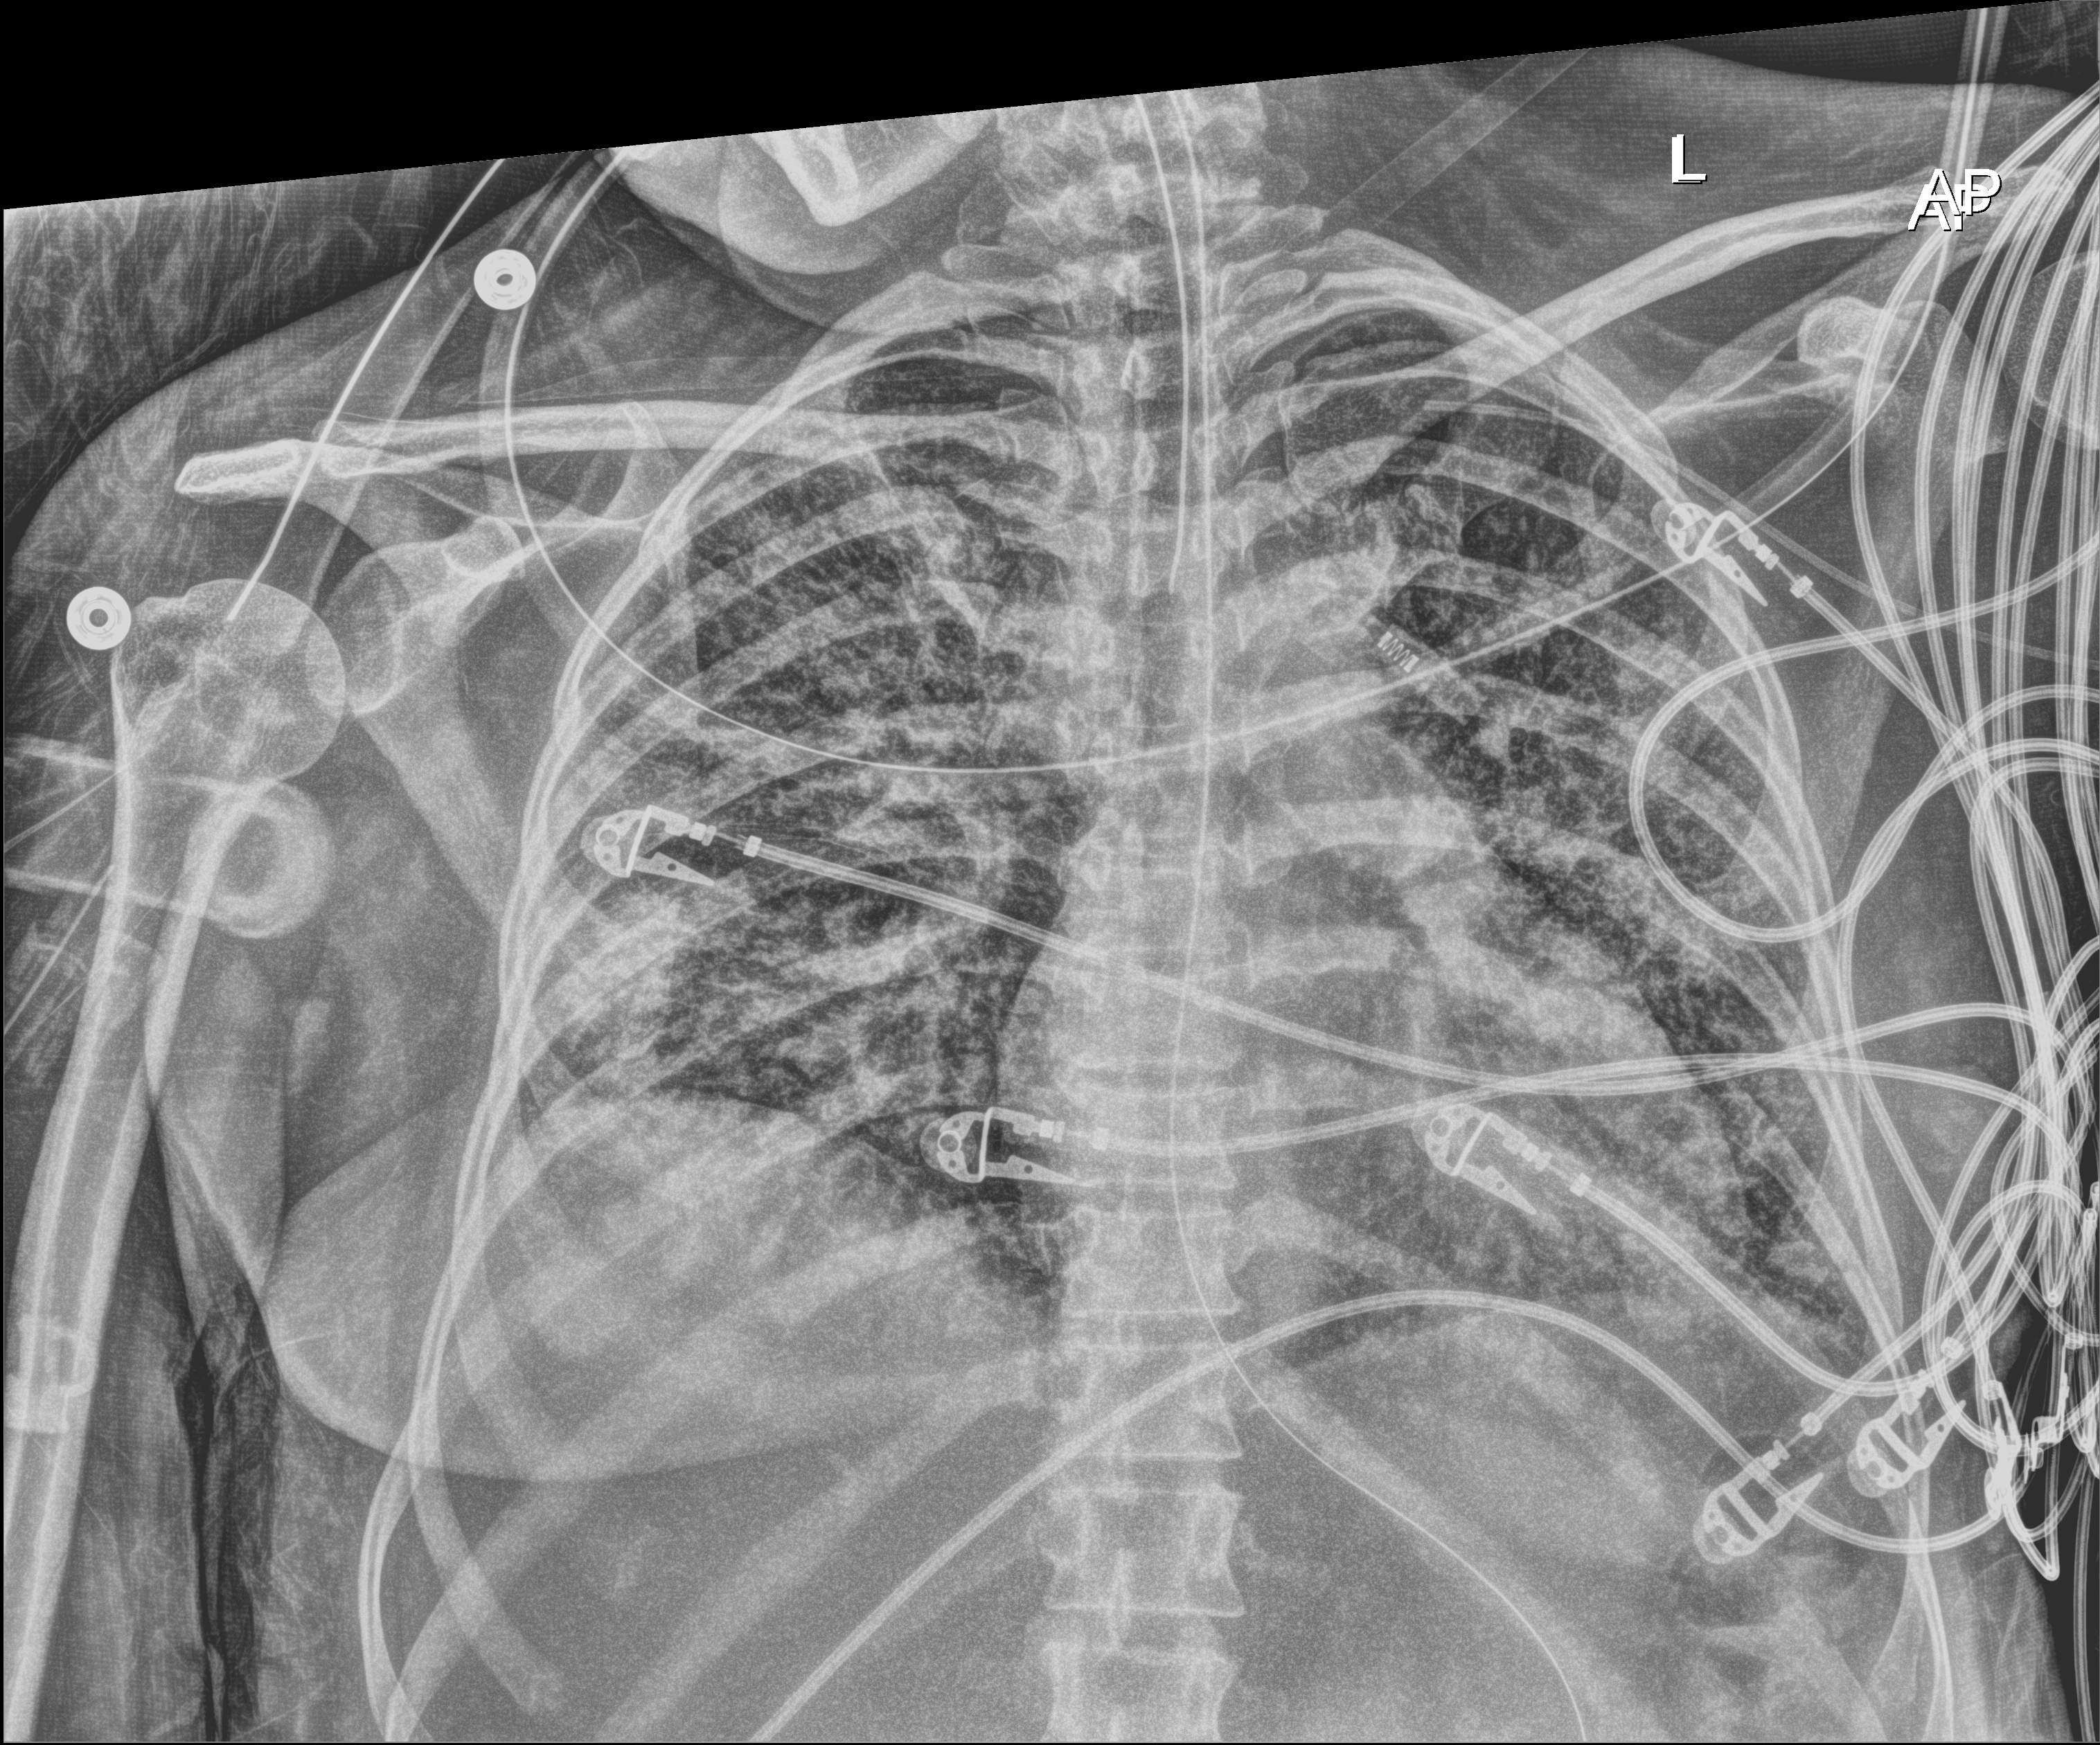
Bedside chest radiograph (digital radiography). Female patient hospitalised with COVID-19, age 18–59 years.
Hospital-stay facts (about this admission, not read from this image; timing relative to this image not recorded):
- smoking status (admission record): former
- mechanically ventilated during this hospital stay: yes